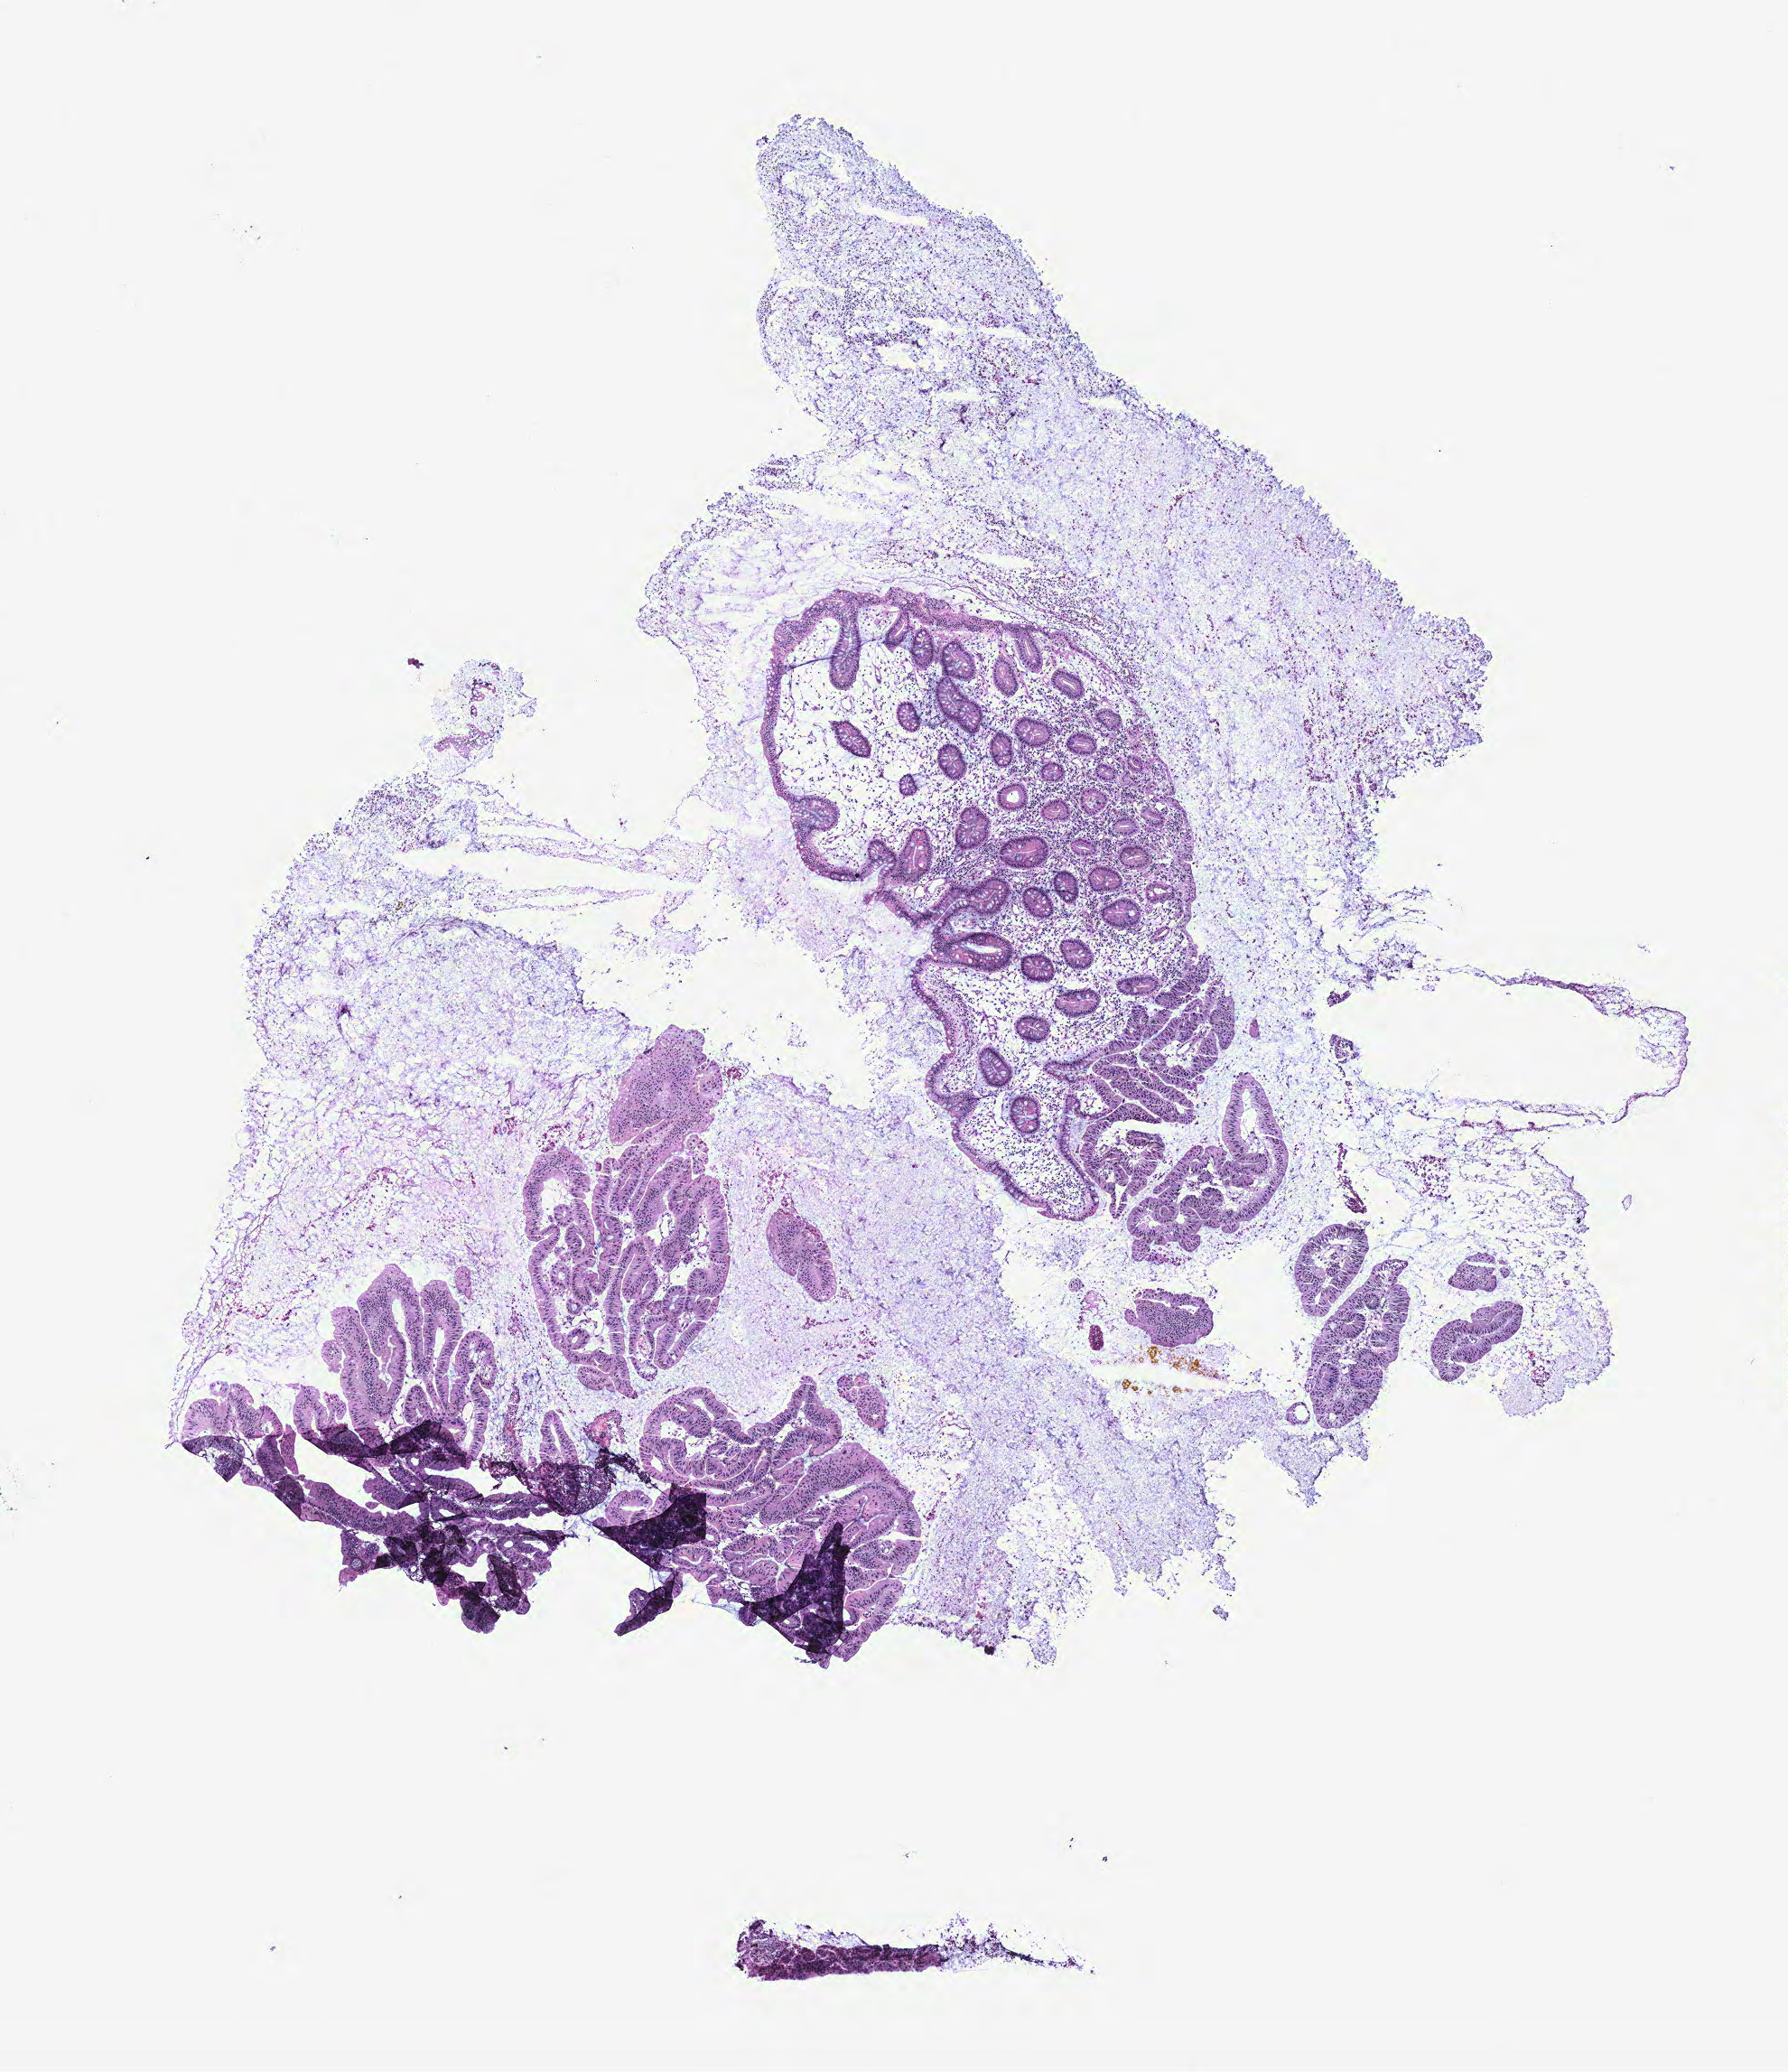
Whole-slide histology image, H&E, a low-resolution overview of the entire scanned area, about 7.9 x 9.2 mm (acquisition: 40x scan), normal (non-tumour) tissue sample, colon. 77-year-old female patient.
• this section: normal (non-tumour) tissue from the same patient
• patient diagnosis: Adenocarcinoma, NOS